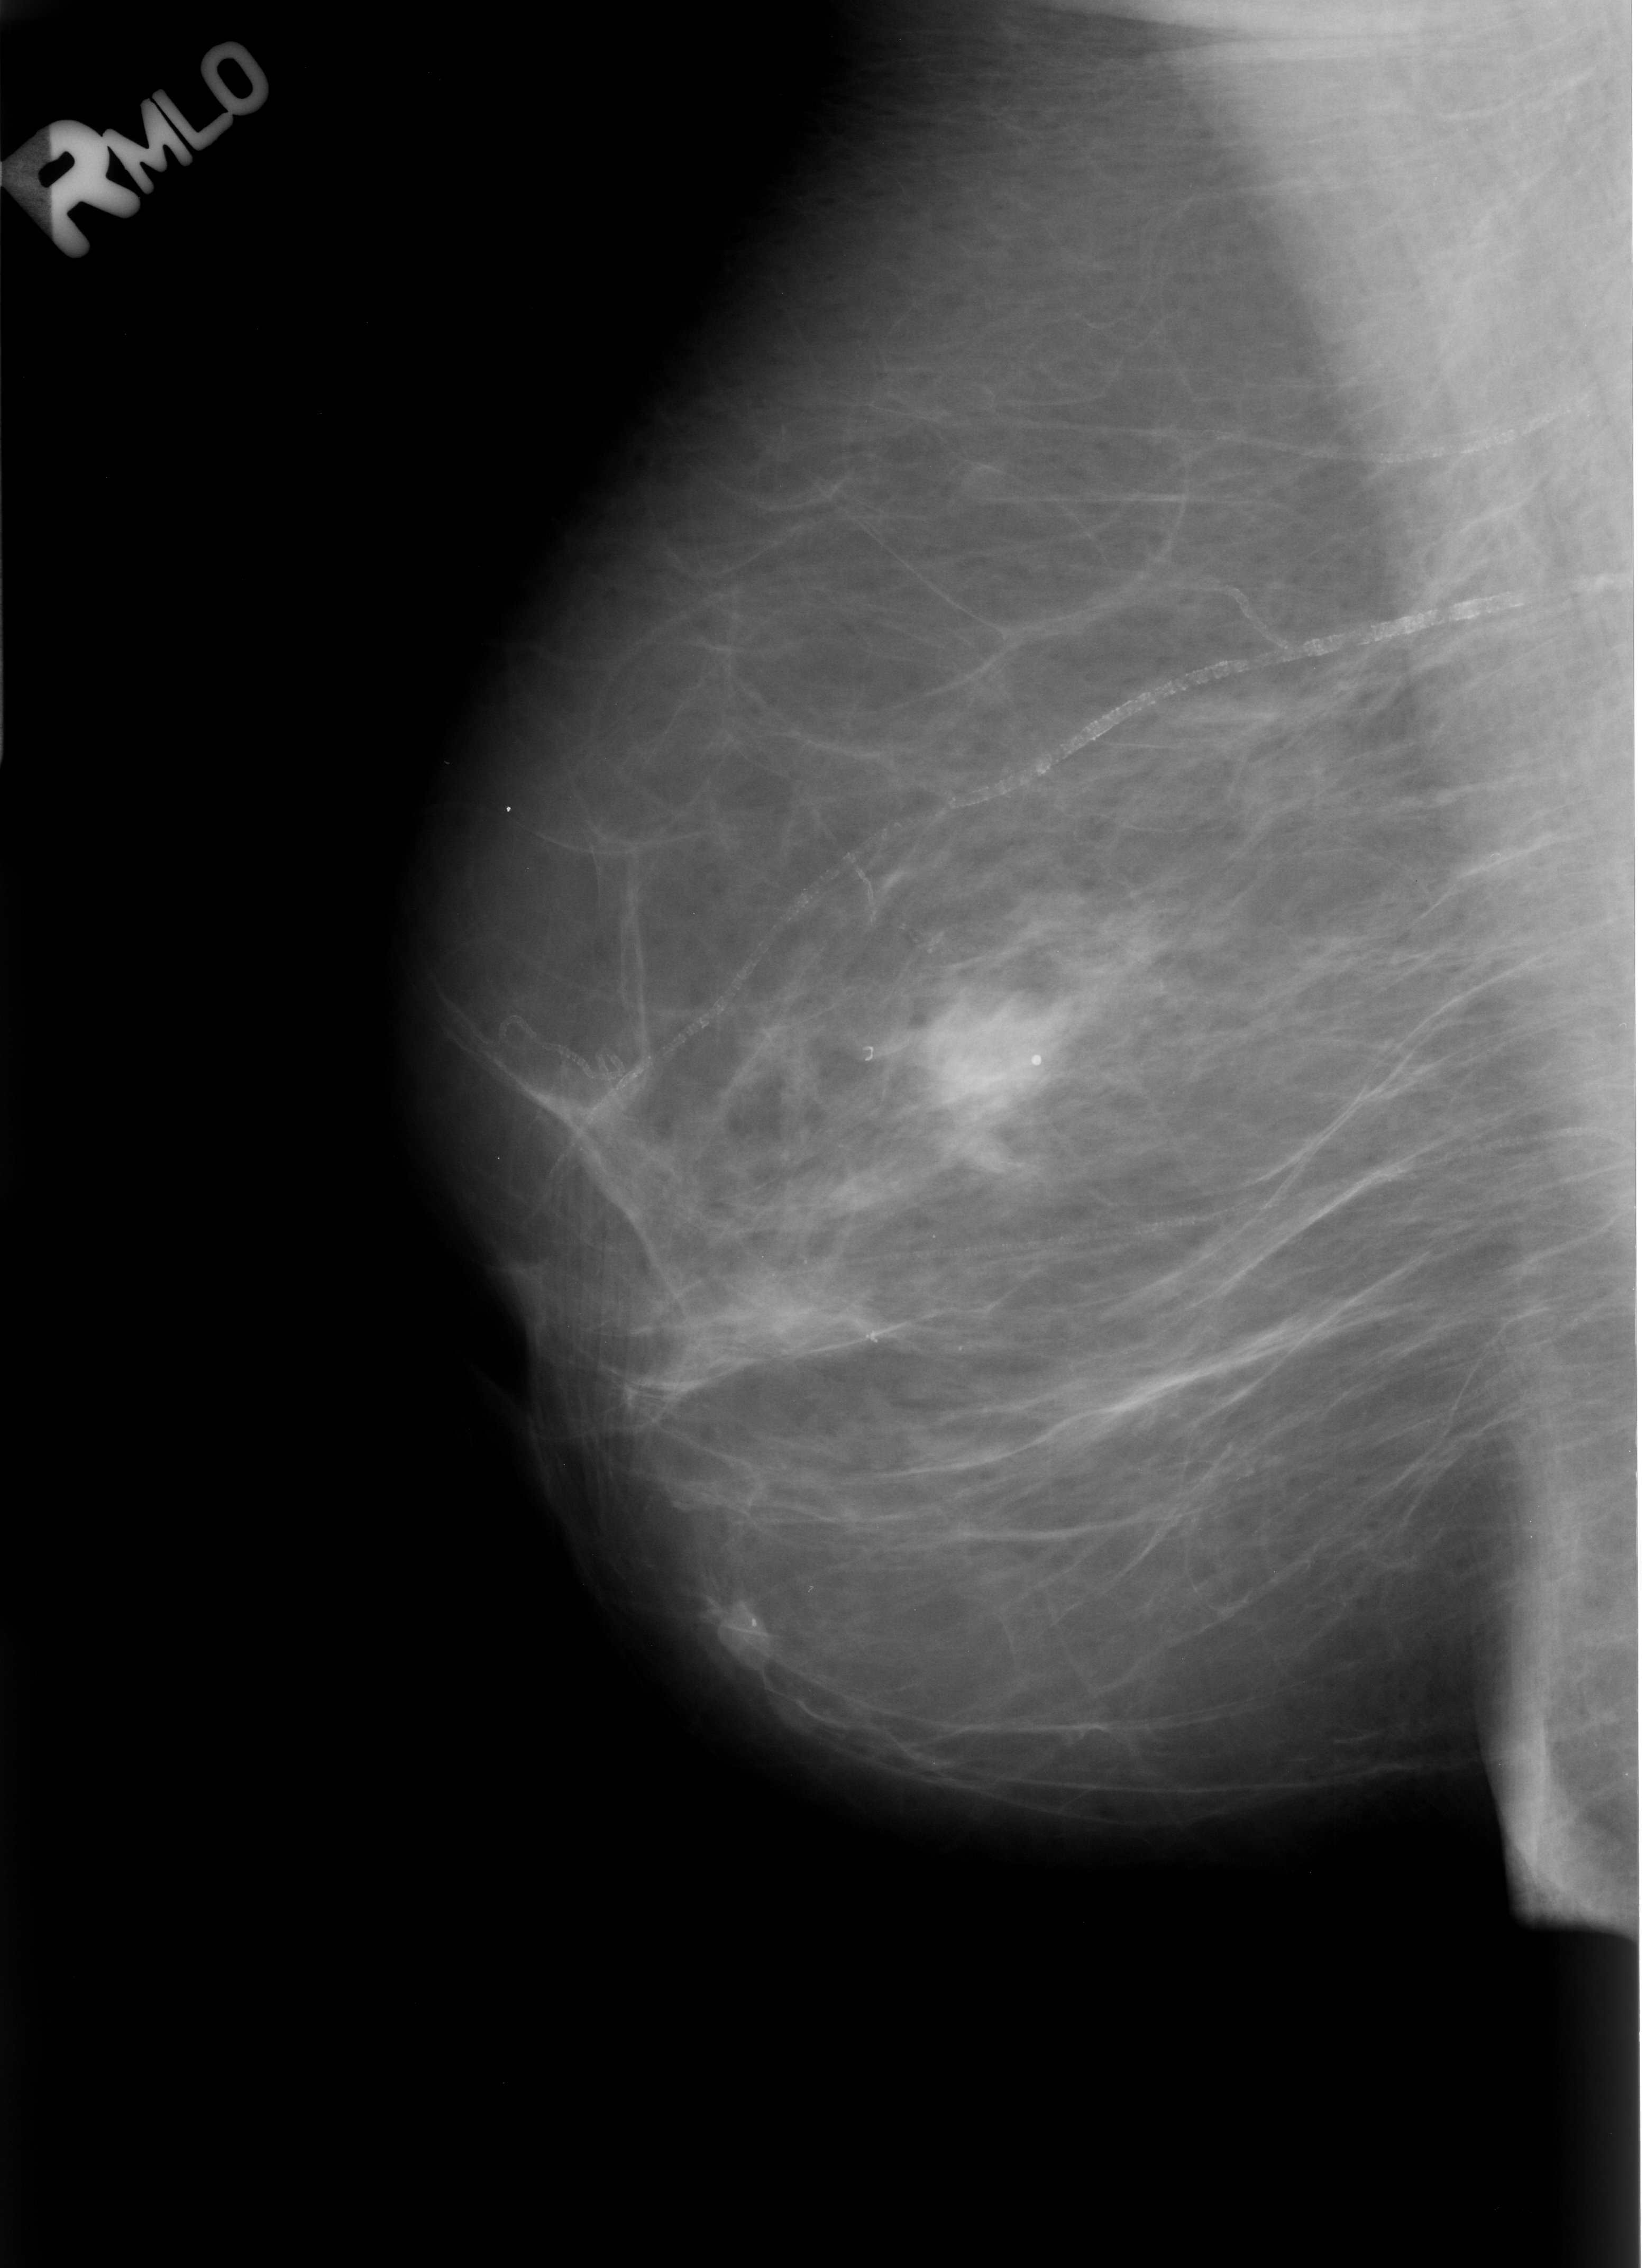
Scanned film-screen mammogram. Right breast. MLO view. Breast composition: scattered fibroglandular densities (BI-RADS density category 2 of 4). 1646 × 2268 image matrix.
Expert-marked regions of interest on this image (one box per marked abnormality):
- mass, shape asymmetric breast tissue; BI-RADS assessment category 2; subtlety rating 5 on a 1 (subtle) to 5 (obvious) scale; benign; no additional work-up was recommended (outcome (as recorded, no biopsy): benign without callback): box from (x=918, y=986) to (x=1073, y=1129) px